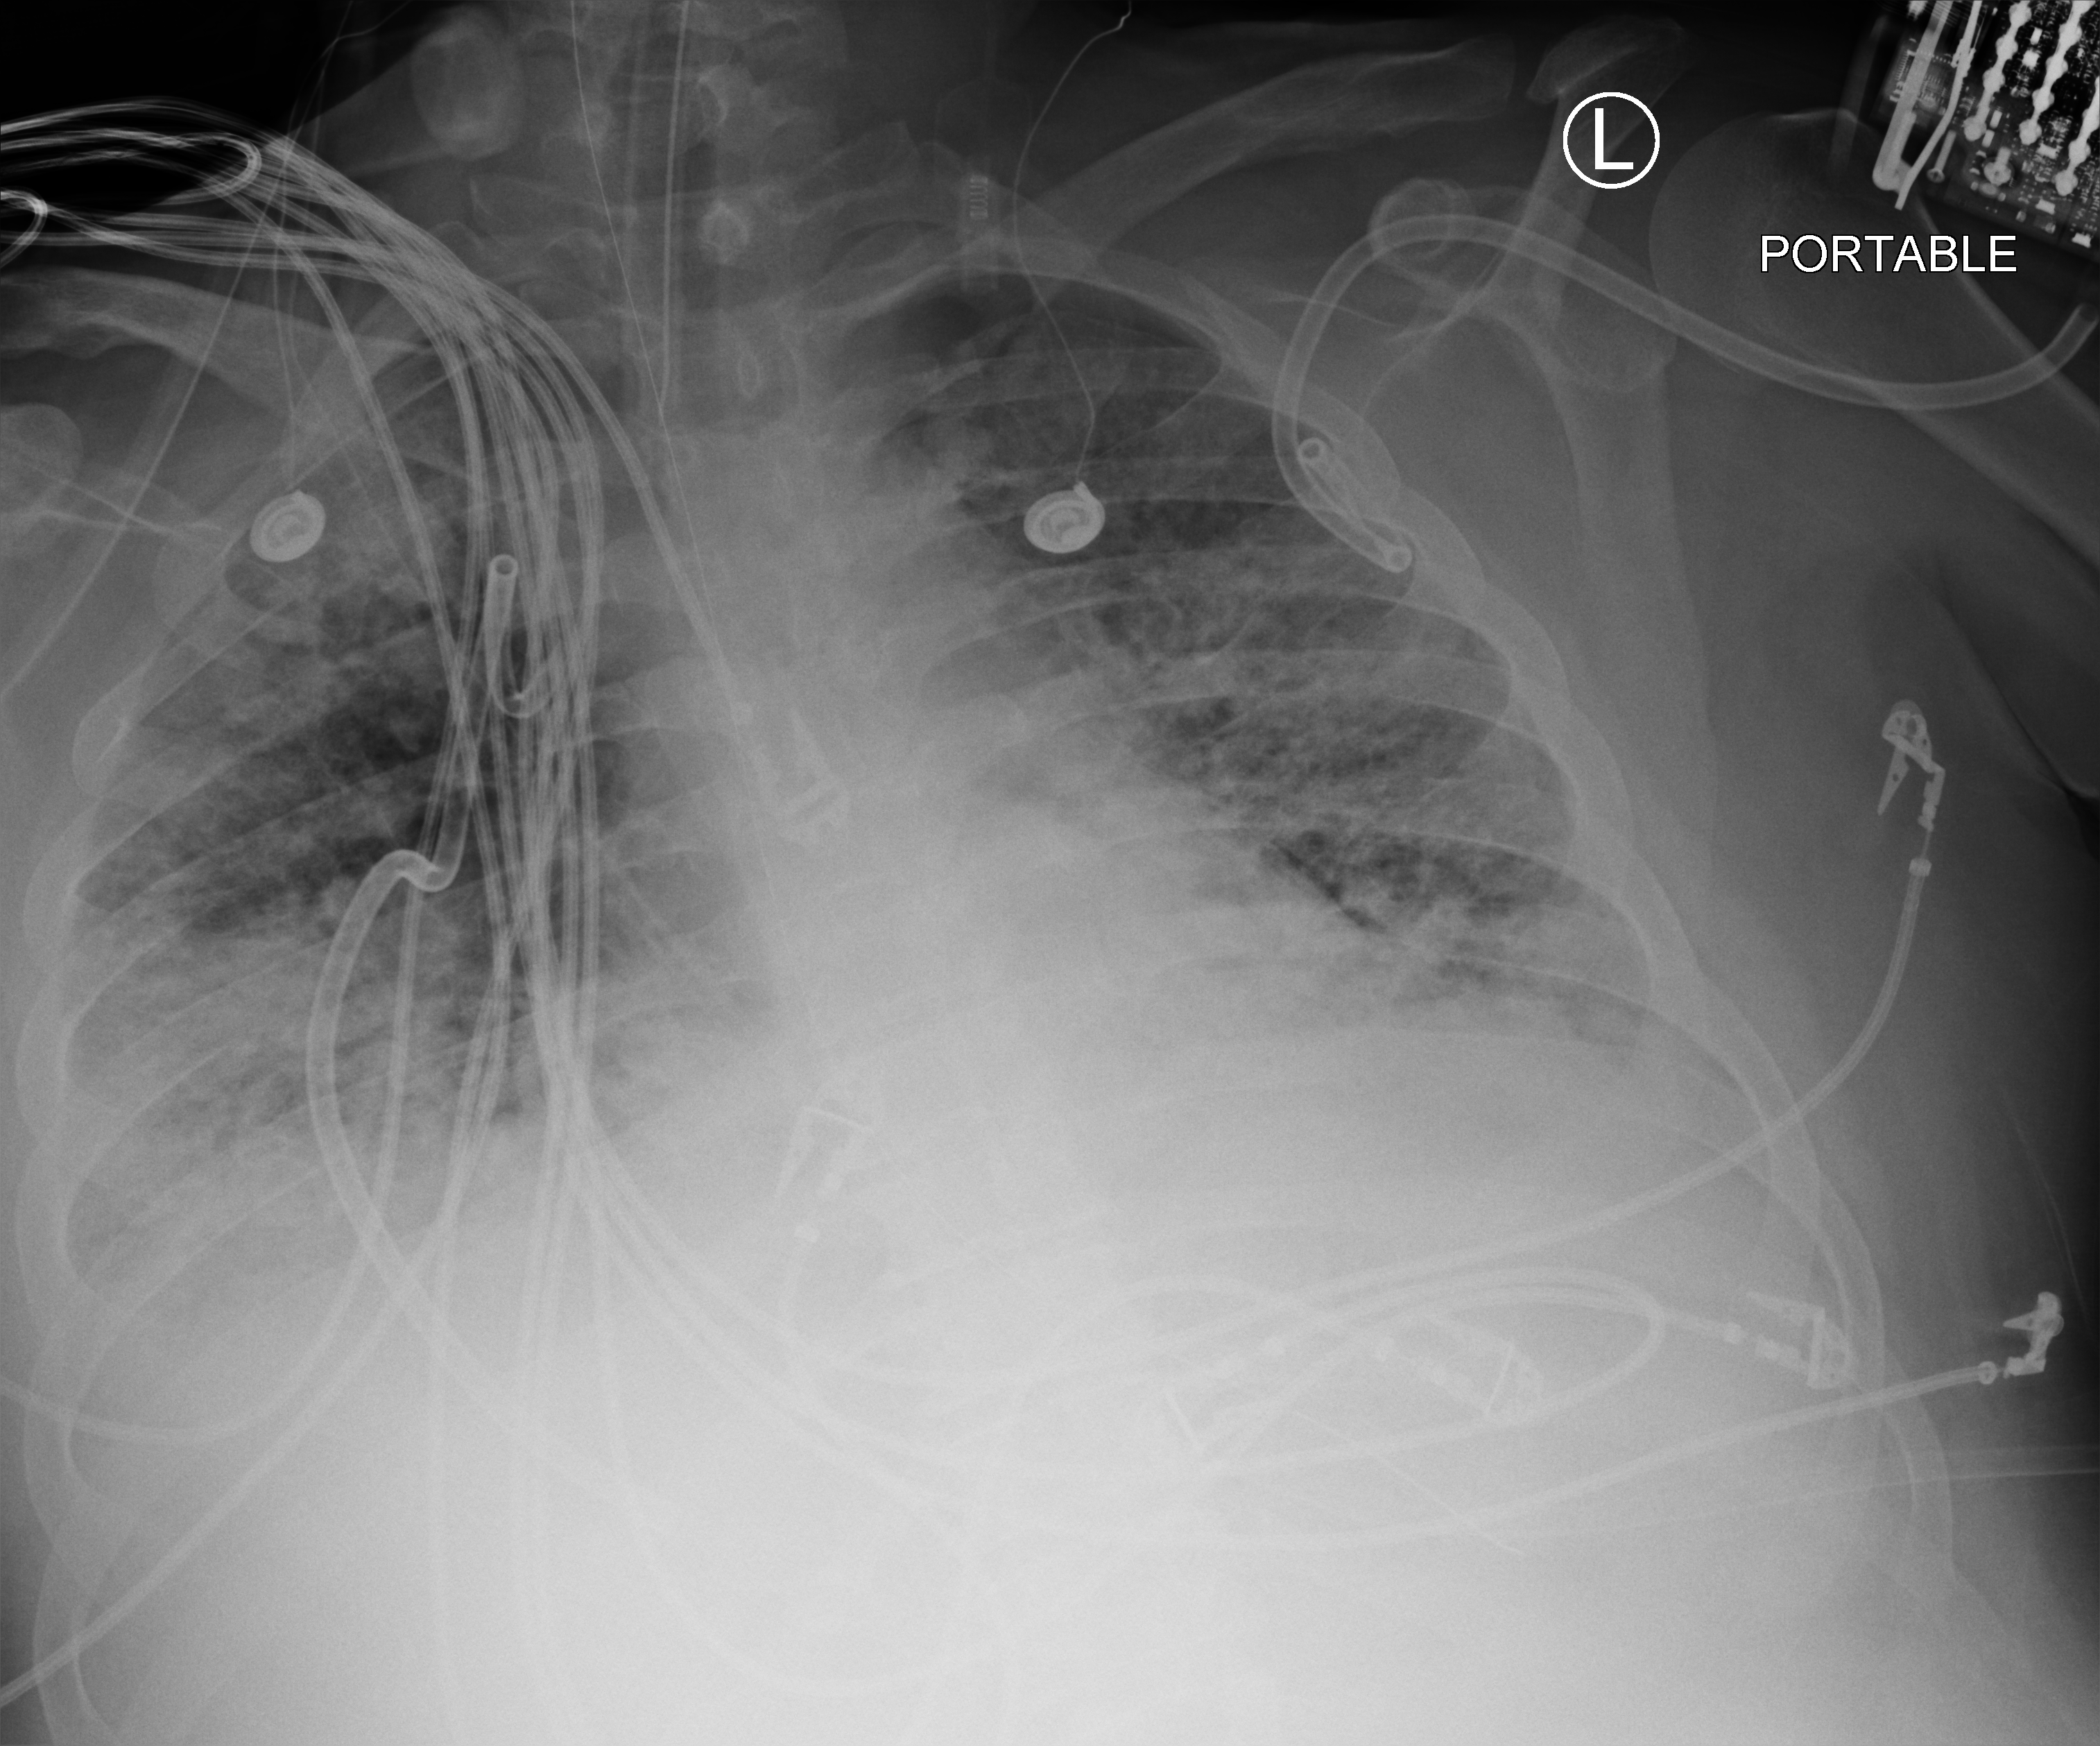
Portable chest radiograph, anteroposterior (AP) projection. Adult patient hospitalised with COVID-19, age 18–59 years.
From the hospital-stay record, not from the radiograph (when in the stay this image was taken is not recorded):
- mechanically ventilated during this hospital stay: yes